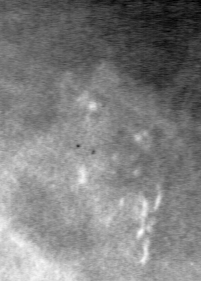
Region of interest cut from a scanned film mammogram (one marked finding), right breast, MLO view, BI-RADS breast density category 3 (scale 1–4).
Finding: calcifications, morphology pleomorphic, distribution clustered; BI-RADS assessment category 4; pathology result (as recorded, not read from the image): benign.